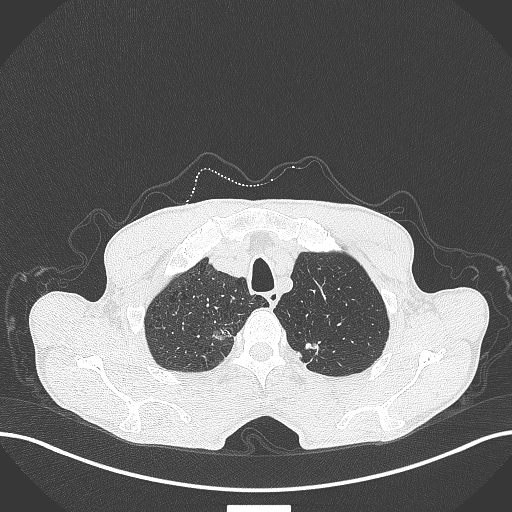
Chest CT, one axial slice. Position 375 of 445 along the scan axis. Reconstruction kernel B70f. 120 kVp. Lung window (W 1500 / L -600 HU). 512 × 512 image matrix. Patient: male, 70 years. Case-level facts recorded for this patient, not image findings: clinical TNM (as recorded): T1a N0 M0; histopathological grade: G1-2.
Annotated regions visible in this slice (rectangle marked by the reading radiologist):
- lung tumour (recorded histology: adenocarcinoma): box from (x=210, y=322) to (x=235, y=343) px